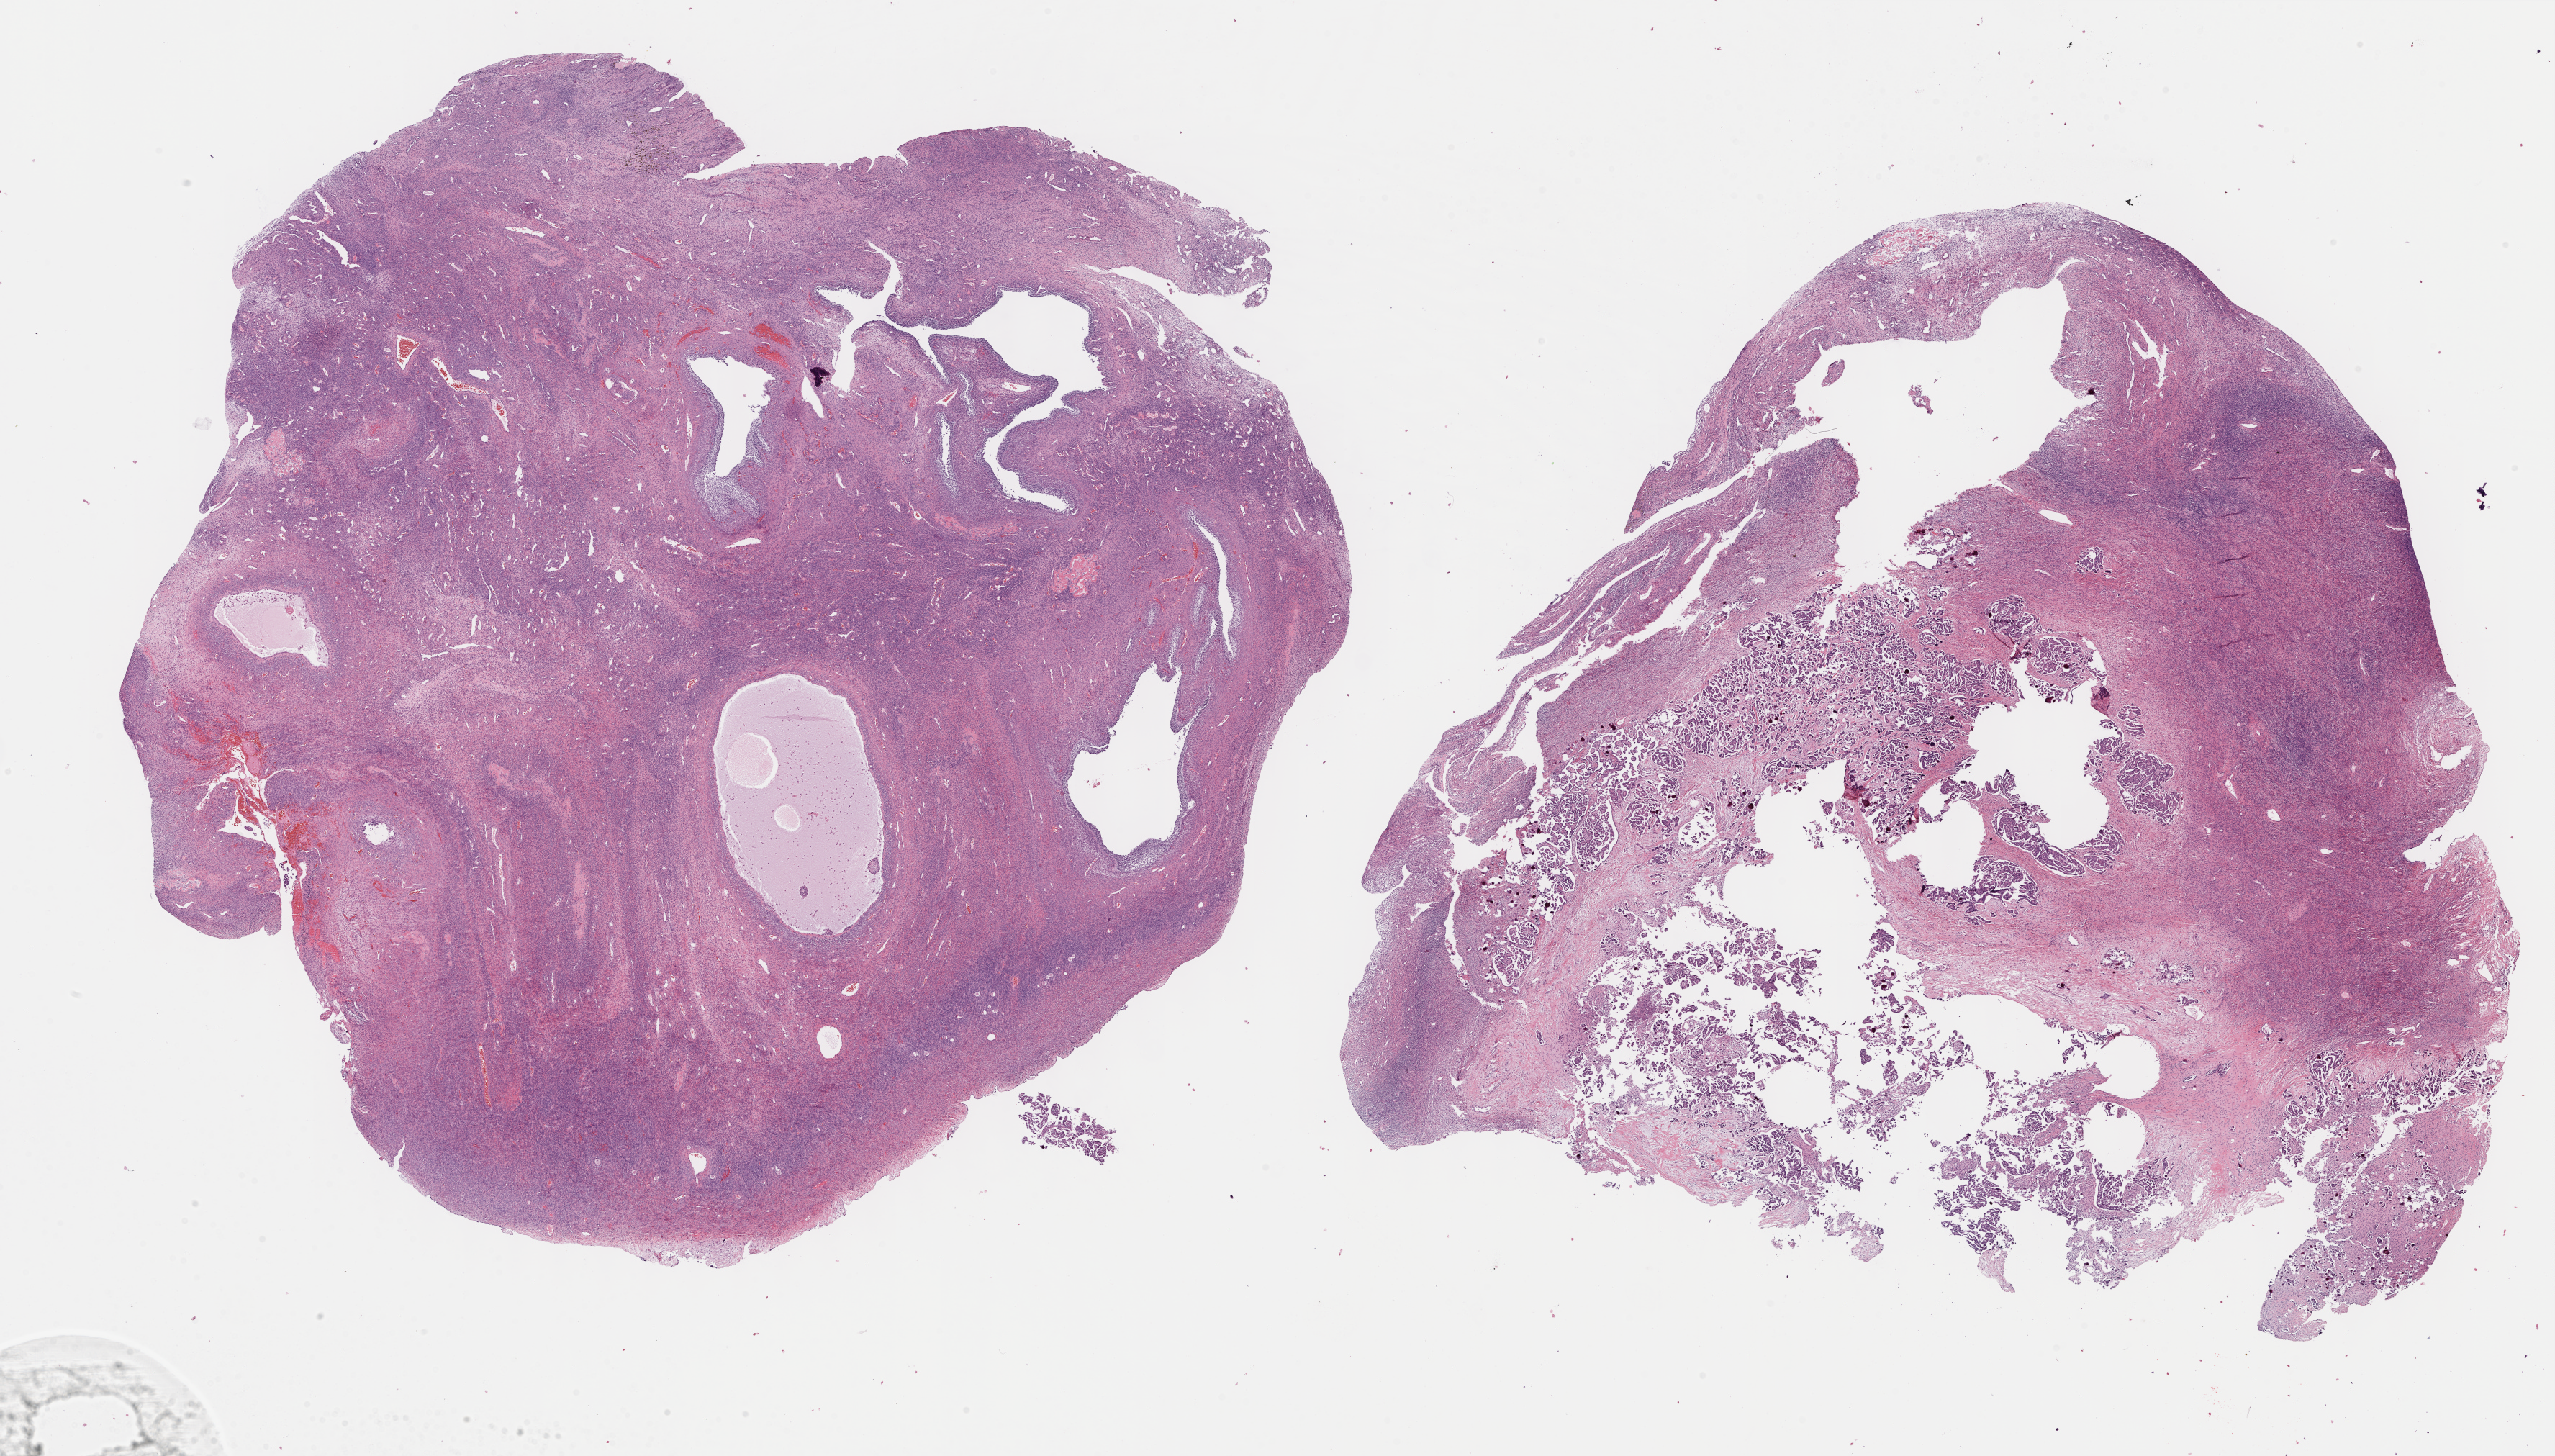
Digitized Hematoxylin and eosin (H&E) stained tissue section (whole slide) — whole scanned area (about 28.7 x 16.3 mm, from a 40x scan) shown as a low-resolution overview, FFPE section, ovary, primary tumour sample. Female, age 37 years at initial diagnosis. Histologic grade: G2 (moderately differentiated).
- diagnosis: Serous cystadenocarcinoma, NOS
- FIGO stage: IV